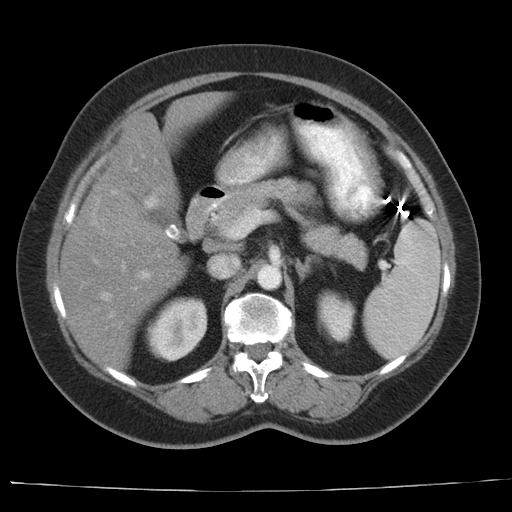
Contrast-enhanced abdominal CT, one axial slice. Intravenous contrast given. Soft-tissue window (W 400 / L 40 HU). 512 × 512 image matrix. Female patient. From the clinical record (not read from this slice): diagnosis: colorectal cancer liver metastases, imaged before liver resection; multiple liver metastases: yes; largest metastasis: 1.8 cm; disease in both lobes: no.
Outlined on this slice (outlined manually by an expert reader):
- hepatic veins: bounding box (x1, y1, x2, y2) in pixels: (101, 191, 116, 300)
- liver: (61, 92, 225, 368)
- planned liver remnant (the part of the liver to remain after resection): (107, 92, 224, 214)
- portal vein (with intrahepatic branches): (94, 155, 155, 278)
- liver metastasis: (98, 191, 162, 241)